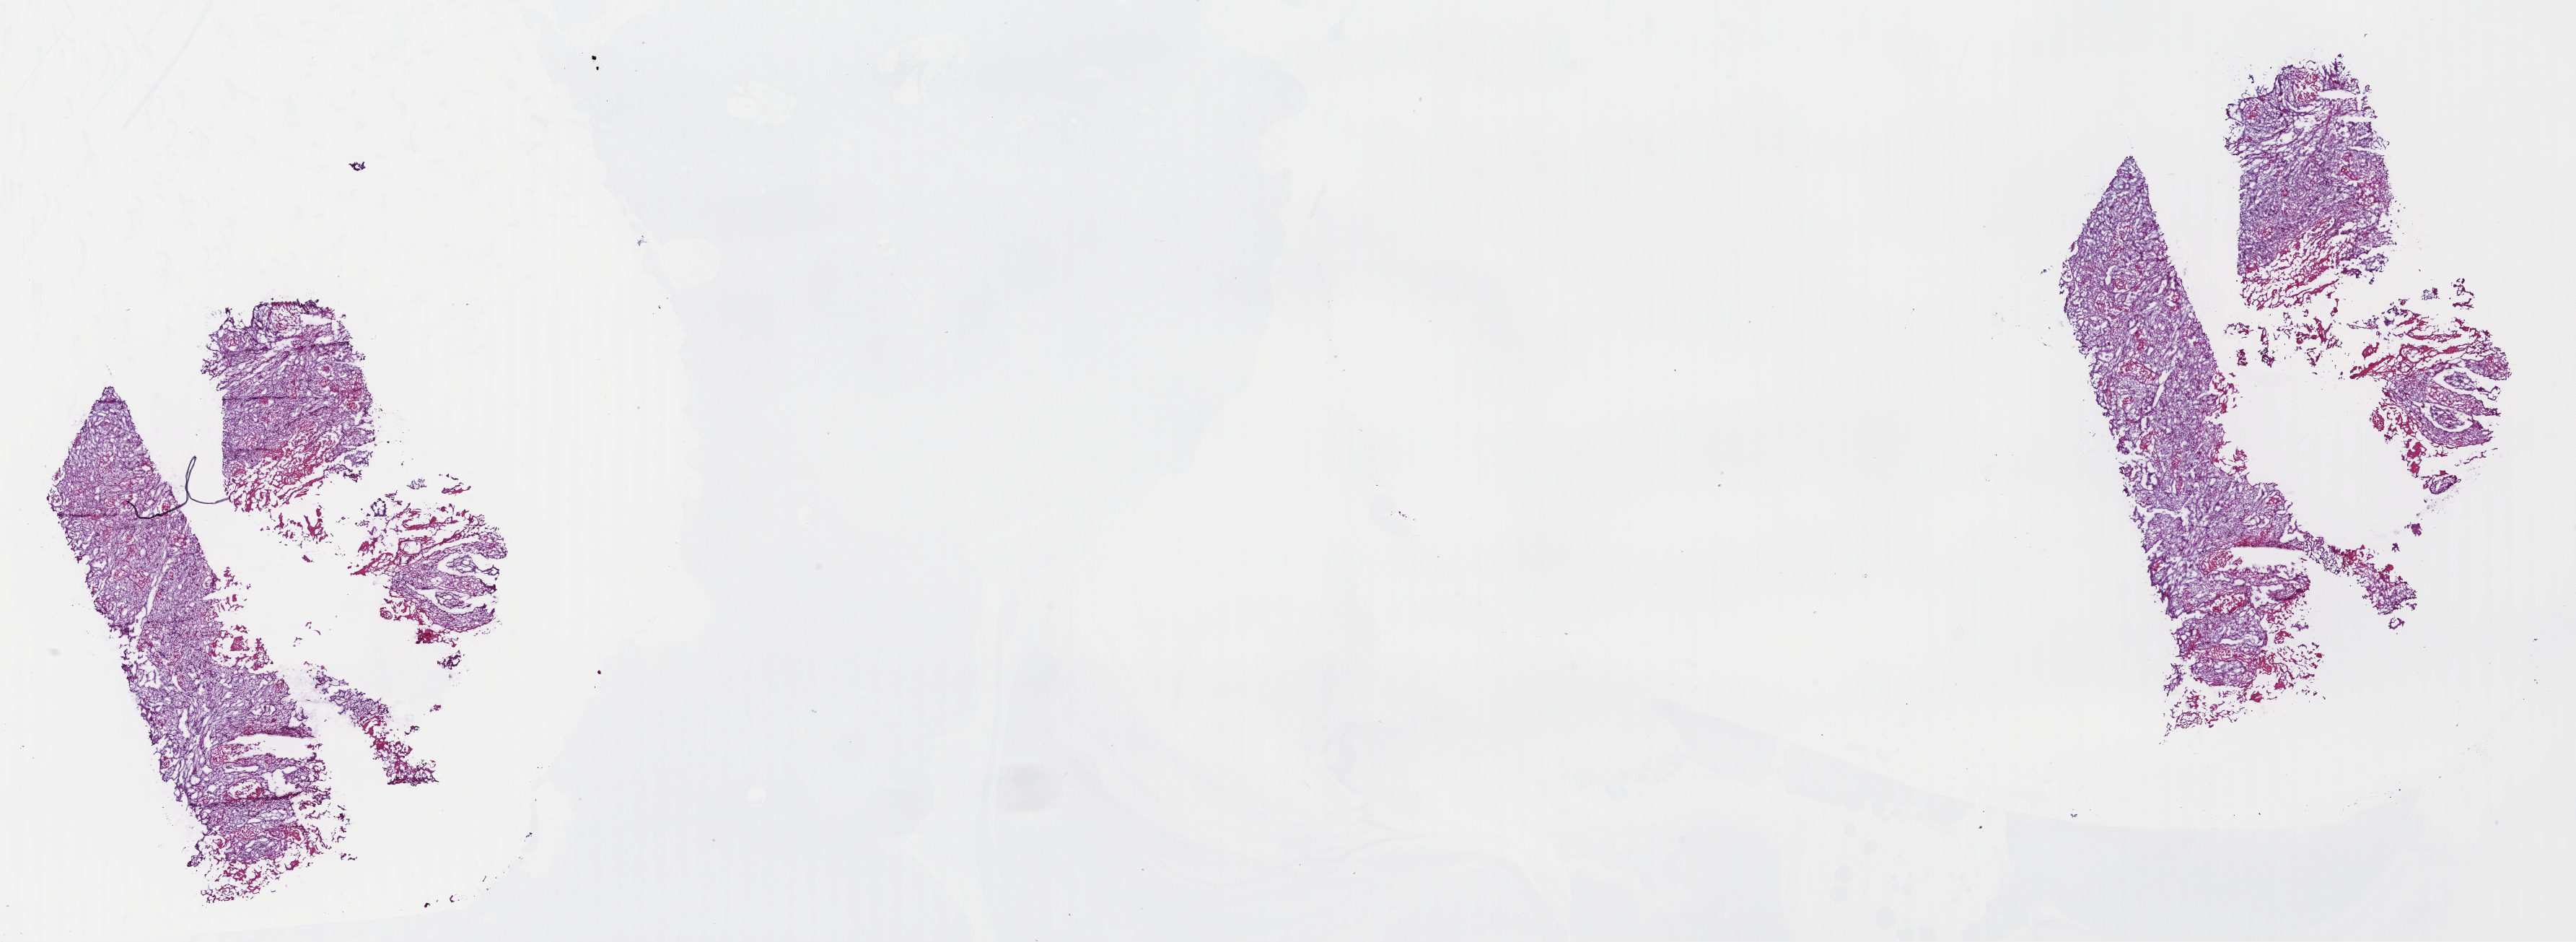
H&E-stained whole-slide image, shown as a low-resolution overview of the whole scanned area (about 28.1 x 10.3 mm, from a 40x scan). Frozen section from the top of the tissue portion. Head and neck, primary tumour sample. Male, age 85 years at initial diagnosis. Histologic grade: G2 (moderately differentiated). Pathologist review of this section (percent, as recorded): tumour cells 65%, tumour nuclei 65%, normal cells 0%, stromal cells 33%, necrosis 2%. Infiltration values recorded for this section: lymphocyte infiltration 2%, monocyte infiltration 1%, neutrophil infiltration 4%.
Diagnosis: Squamous cell carcinoma, NOS (larynx, NOS).